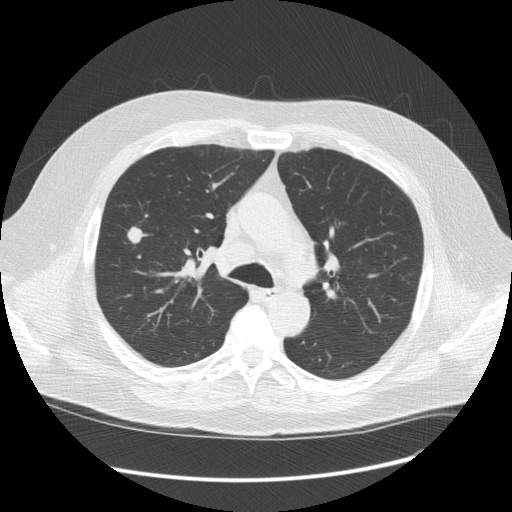
Low-dose screening chest CT, one axial slice. Slice 87 of 128 in the series (ordered by position). Reconstruction kernel STANDARD. 120 kVp. Lung window (W 1500 / L -600 HU). 2.5 mm slice thickness. 512 × 512 image matrix.
Outlined on this slice (manually delineated by an expert):
- lesion 1 (tumor, upper lobe of right lung): bounding box [x1, y1, x2, y2] px = [128, 227, 144, 243]